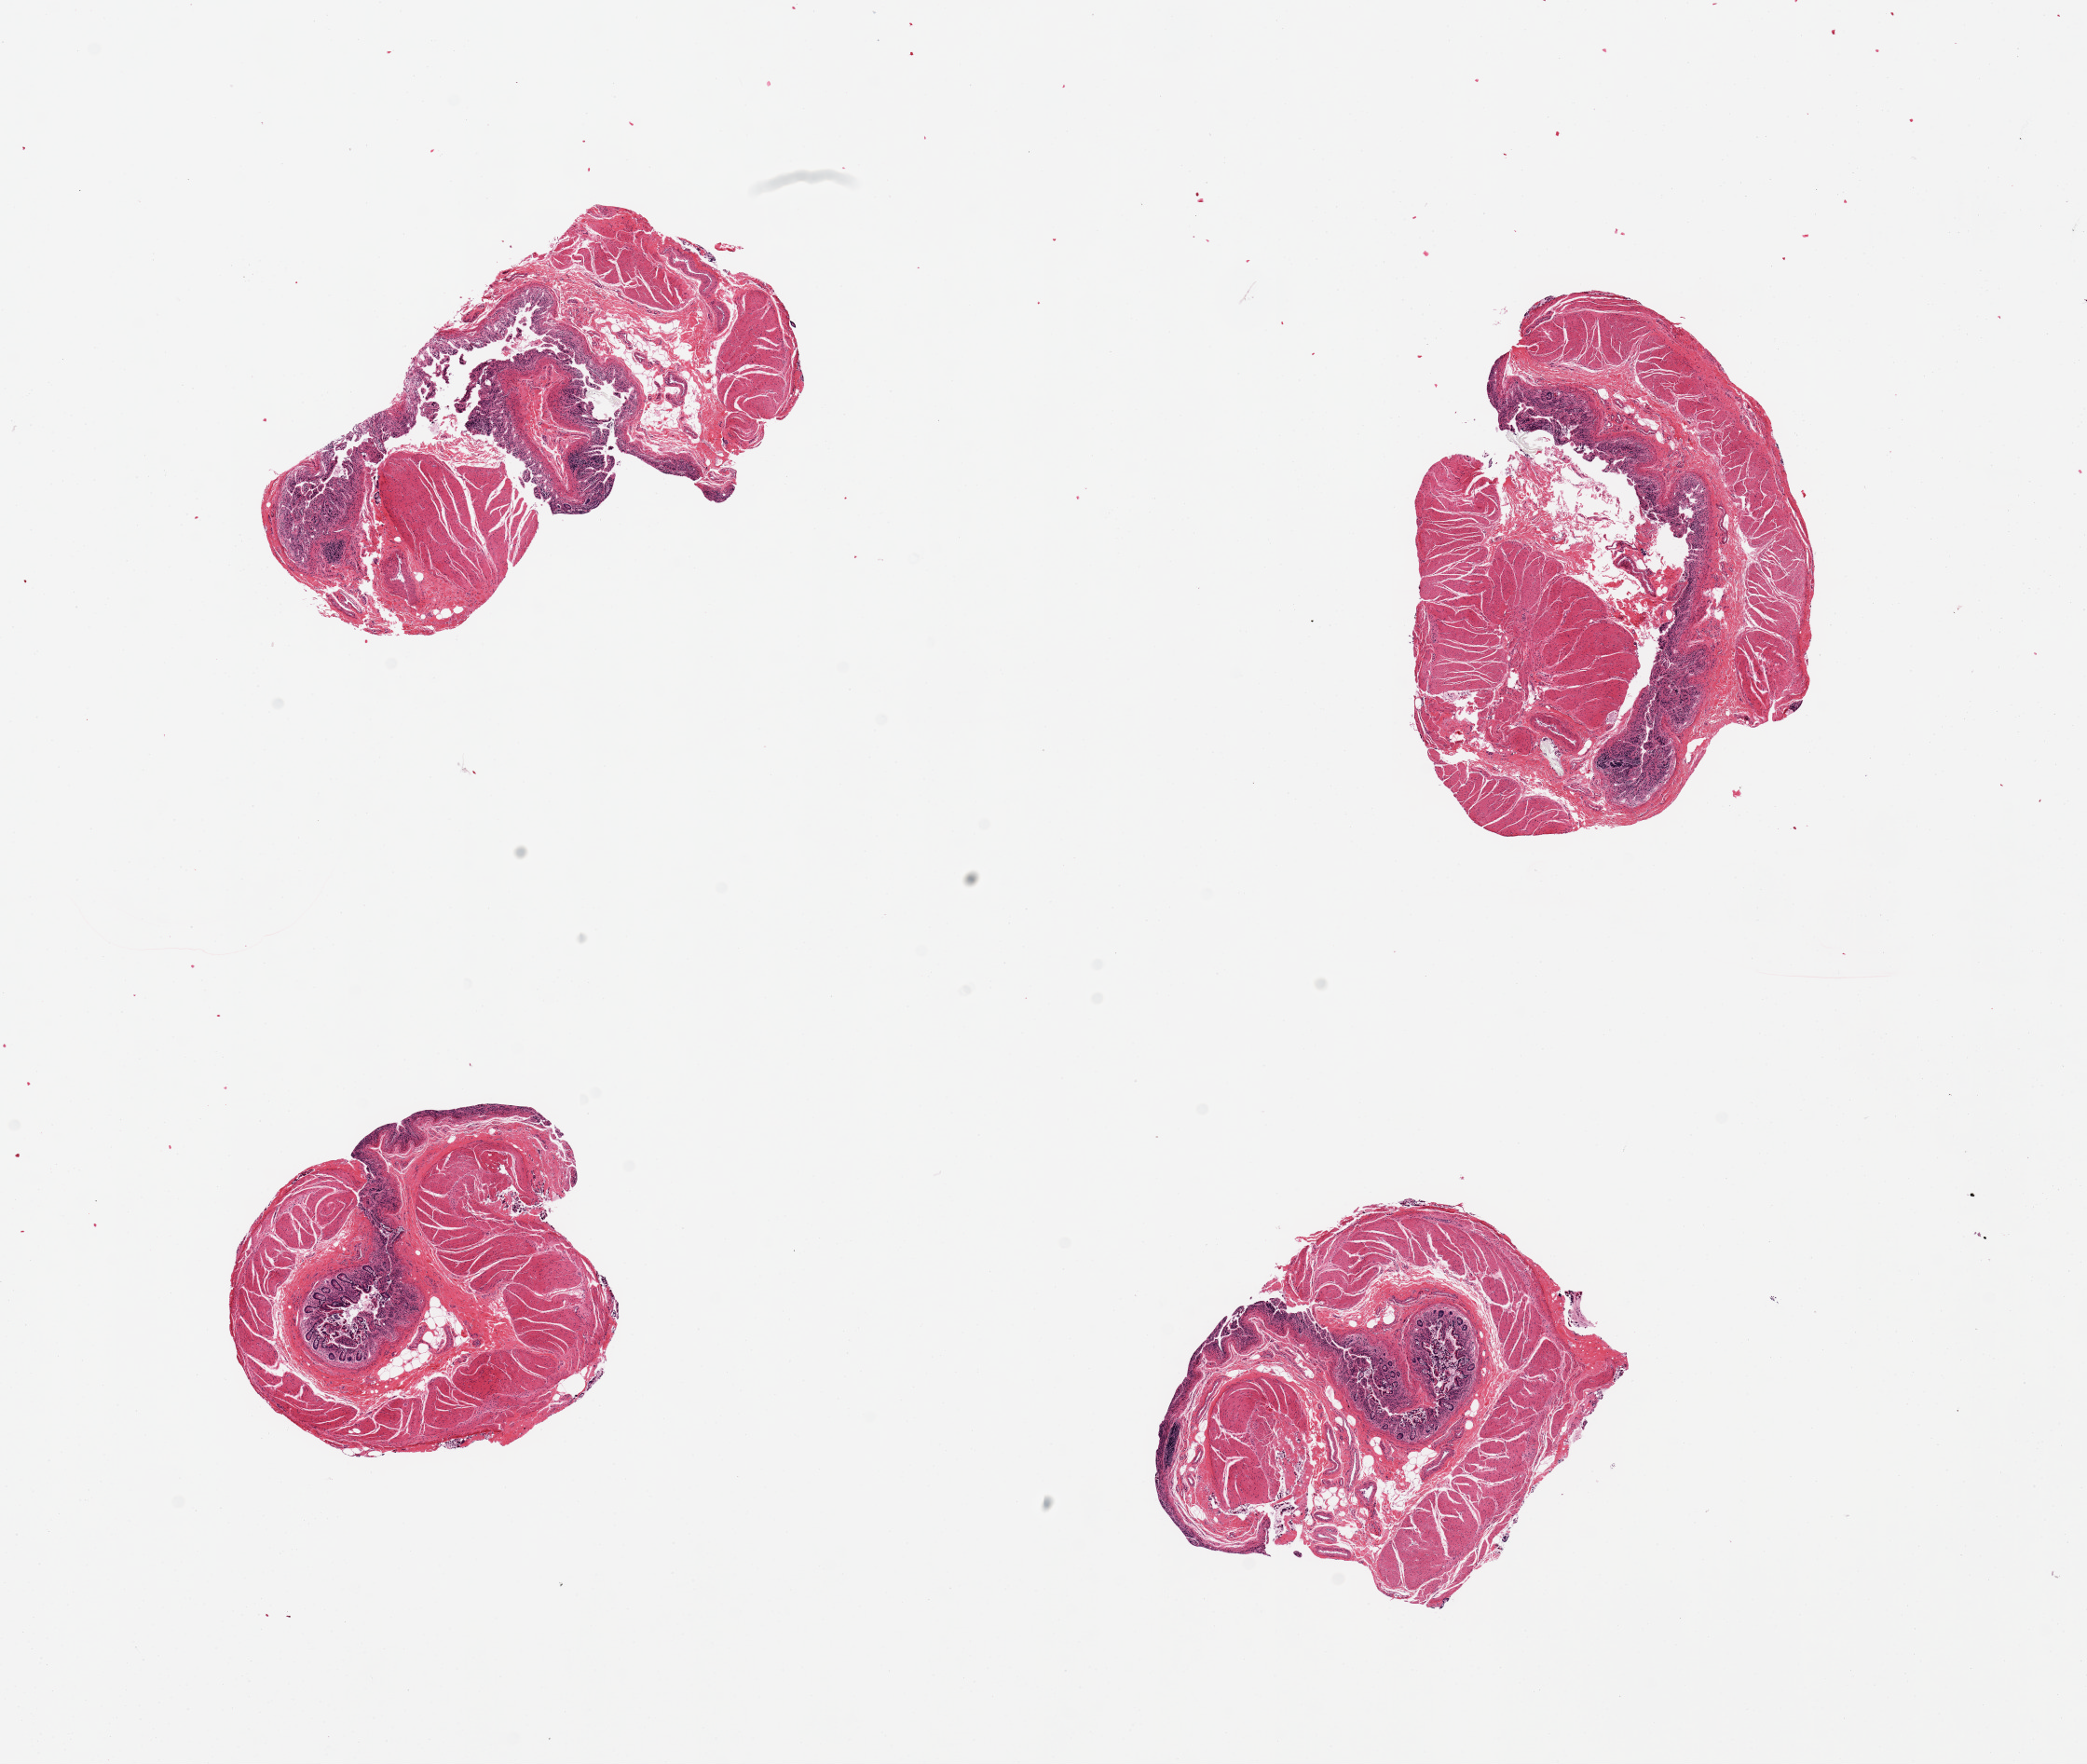
Digitized hematoxylin and eosin (H&E)-stained section, a low-resolution overview of the entire scanned area, about 17.7 x 15.0 mm; PAXgene-fixed, paraffin-embedded tissue; section of ileum (target tissue); donor tissue sample. Donor sex: female.
• pathologist's review note for this sample: 4 pieces, muscularis and autolyzed mucosa with inadequate lymphoid tissue